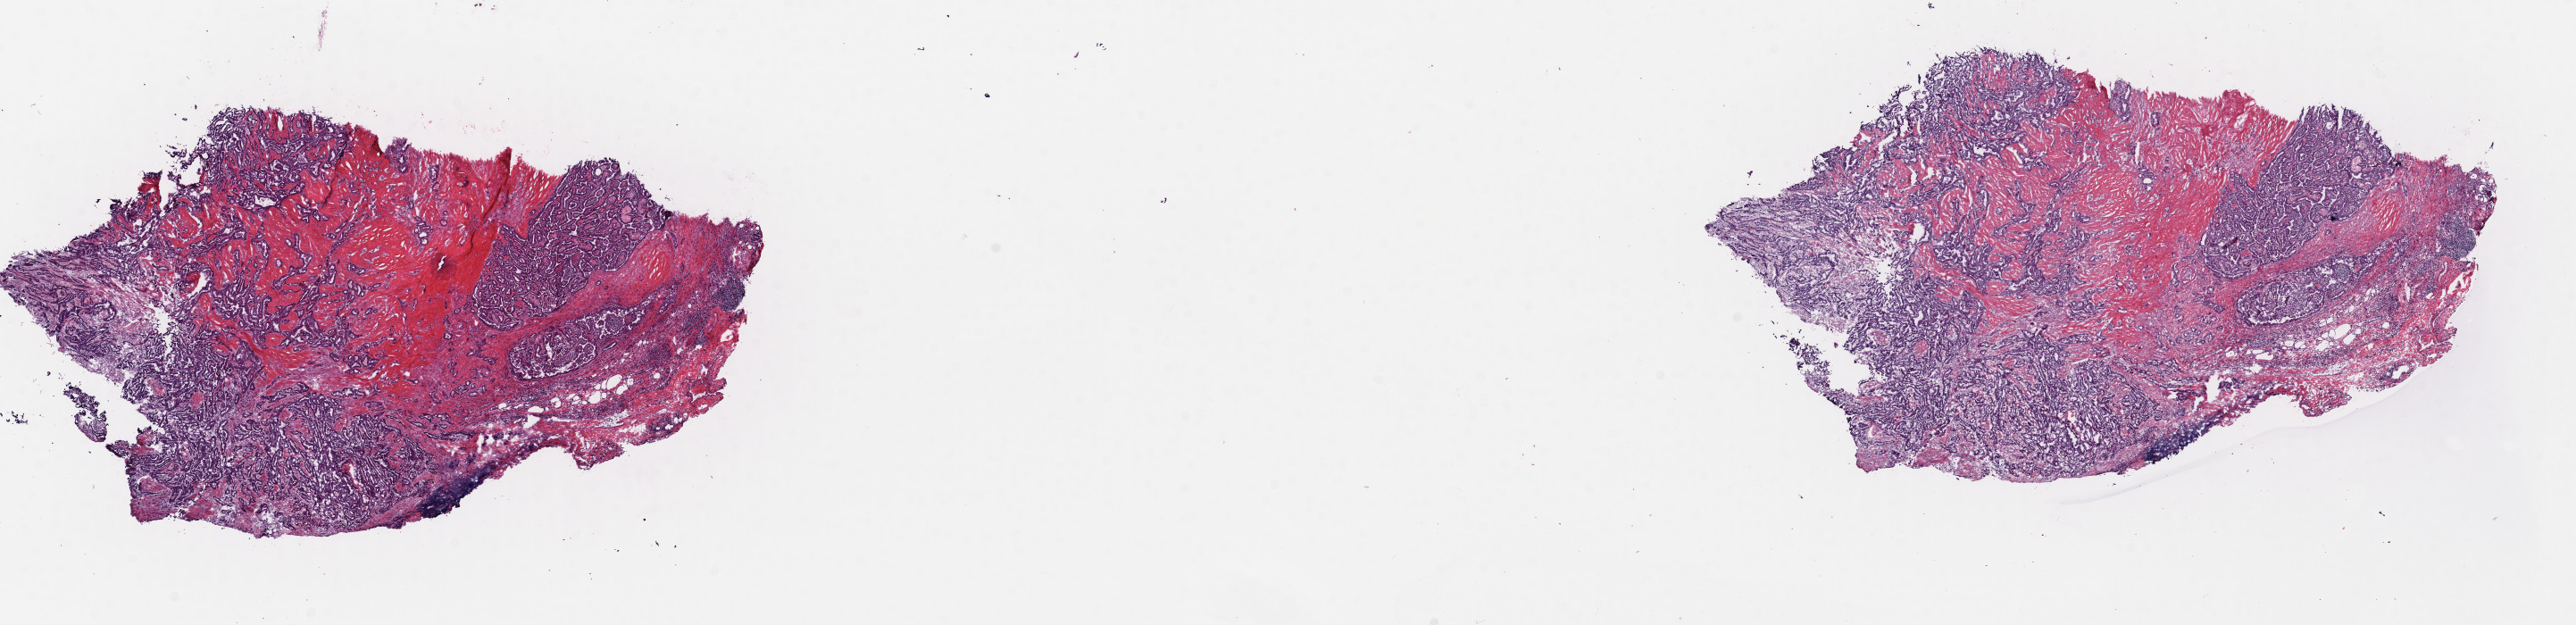
Hematoxylin and eosin (H&E) stained whole-slide image — a low-resolution overview of the entire scanned area, about 22.8 x 5.5 mm (slide scanned at 40x). Frozen section. Sample: primary tumour, thyroid. Female patient; age at initial diagnosis 61 years. Composition of this section per pathologist review: tumour cells 65%, tumour nuclei 75%, normal cells 10%, stromal cells 25%, necrosis 0%. Inflammatory infiltration, as recorded: lymphocyte infiltration 1%, monocyte infiltration 0%, neutrophil infiltration 0%.
AJCC pathologic stage: III. Lymph nodes positive (case pathology): 1 of 6 examined. Laterality: left. TNM: T3 N1a M0. Diagnosis: Papillary carcinoma, columnar cell (thyroid gland).